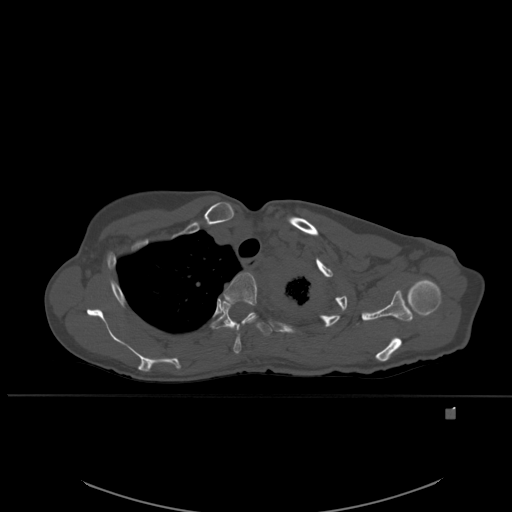
CT including the spine, one axial slice; slice 419 of 537 in the series (ordered by position); bone window (W 1800 / L 400 HU); 1.5 mm slice thickness; 512 × 512 image matrix, field of view 440 × 440 mm. Patient: female, 45 years. Case-level facts recorded for this patient, not image findings: primary cancer: lung.
Outlined on this slice (semi-automatically segmented with operator editing):
- T3 vertebra: bounding box (x1, y1, x2, y2) in pixels: (224, 272, 258, 354)
- T4 vertebra: (211, 299, 274, 336)